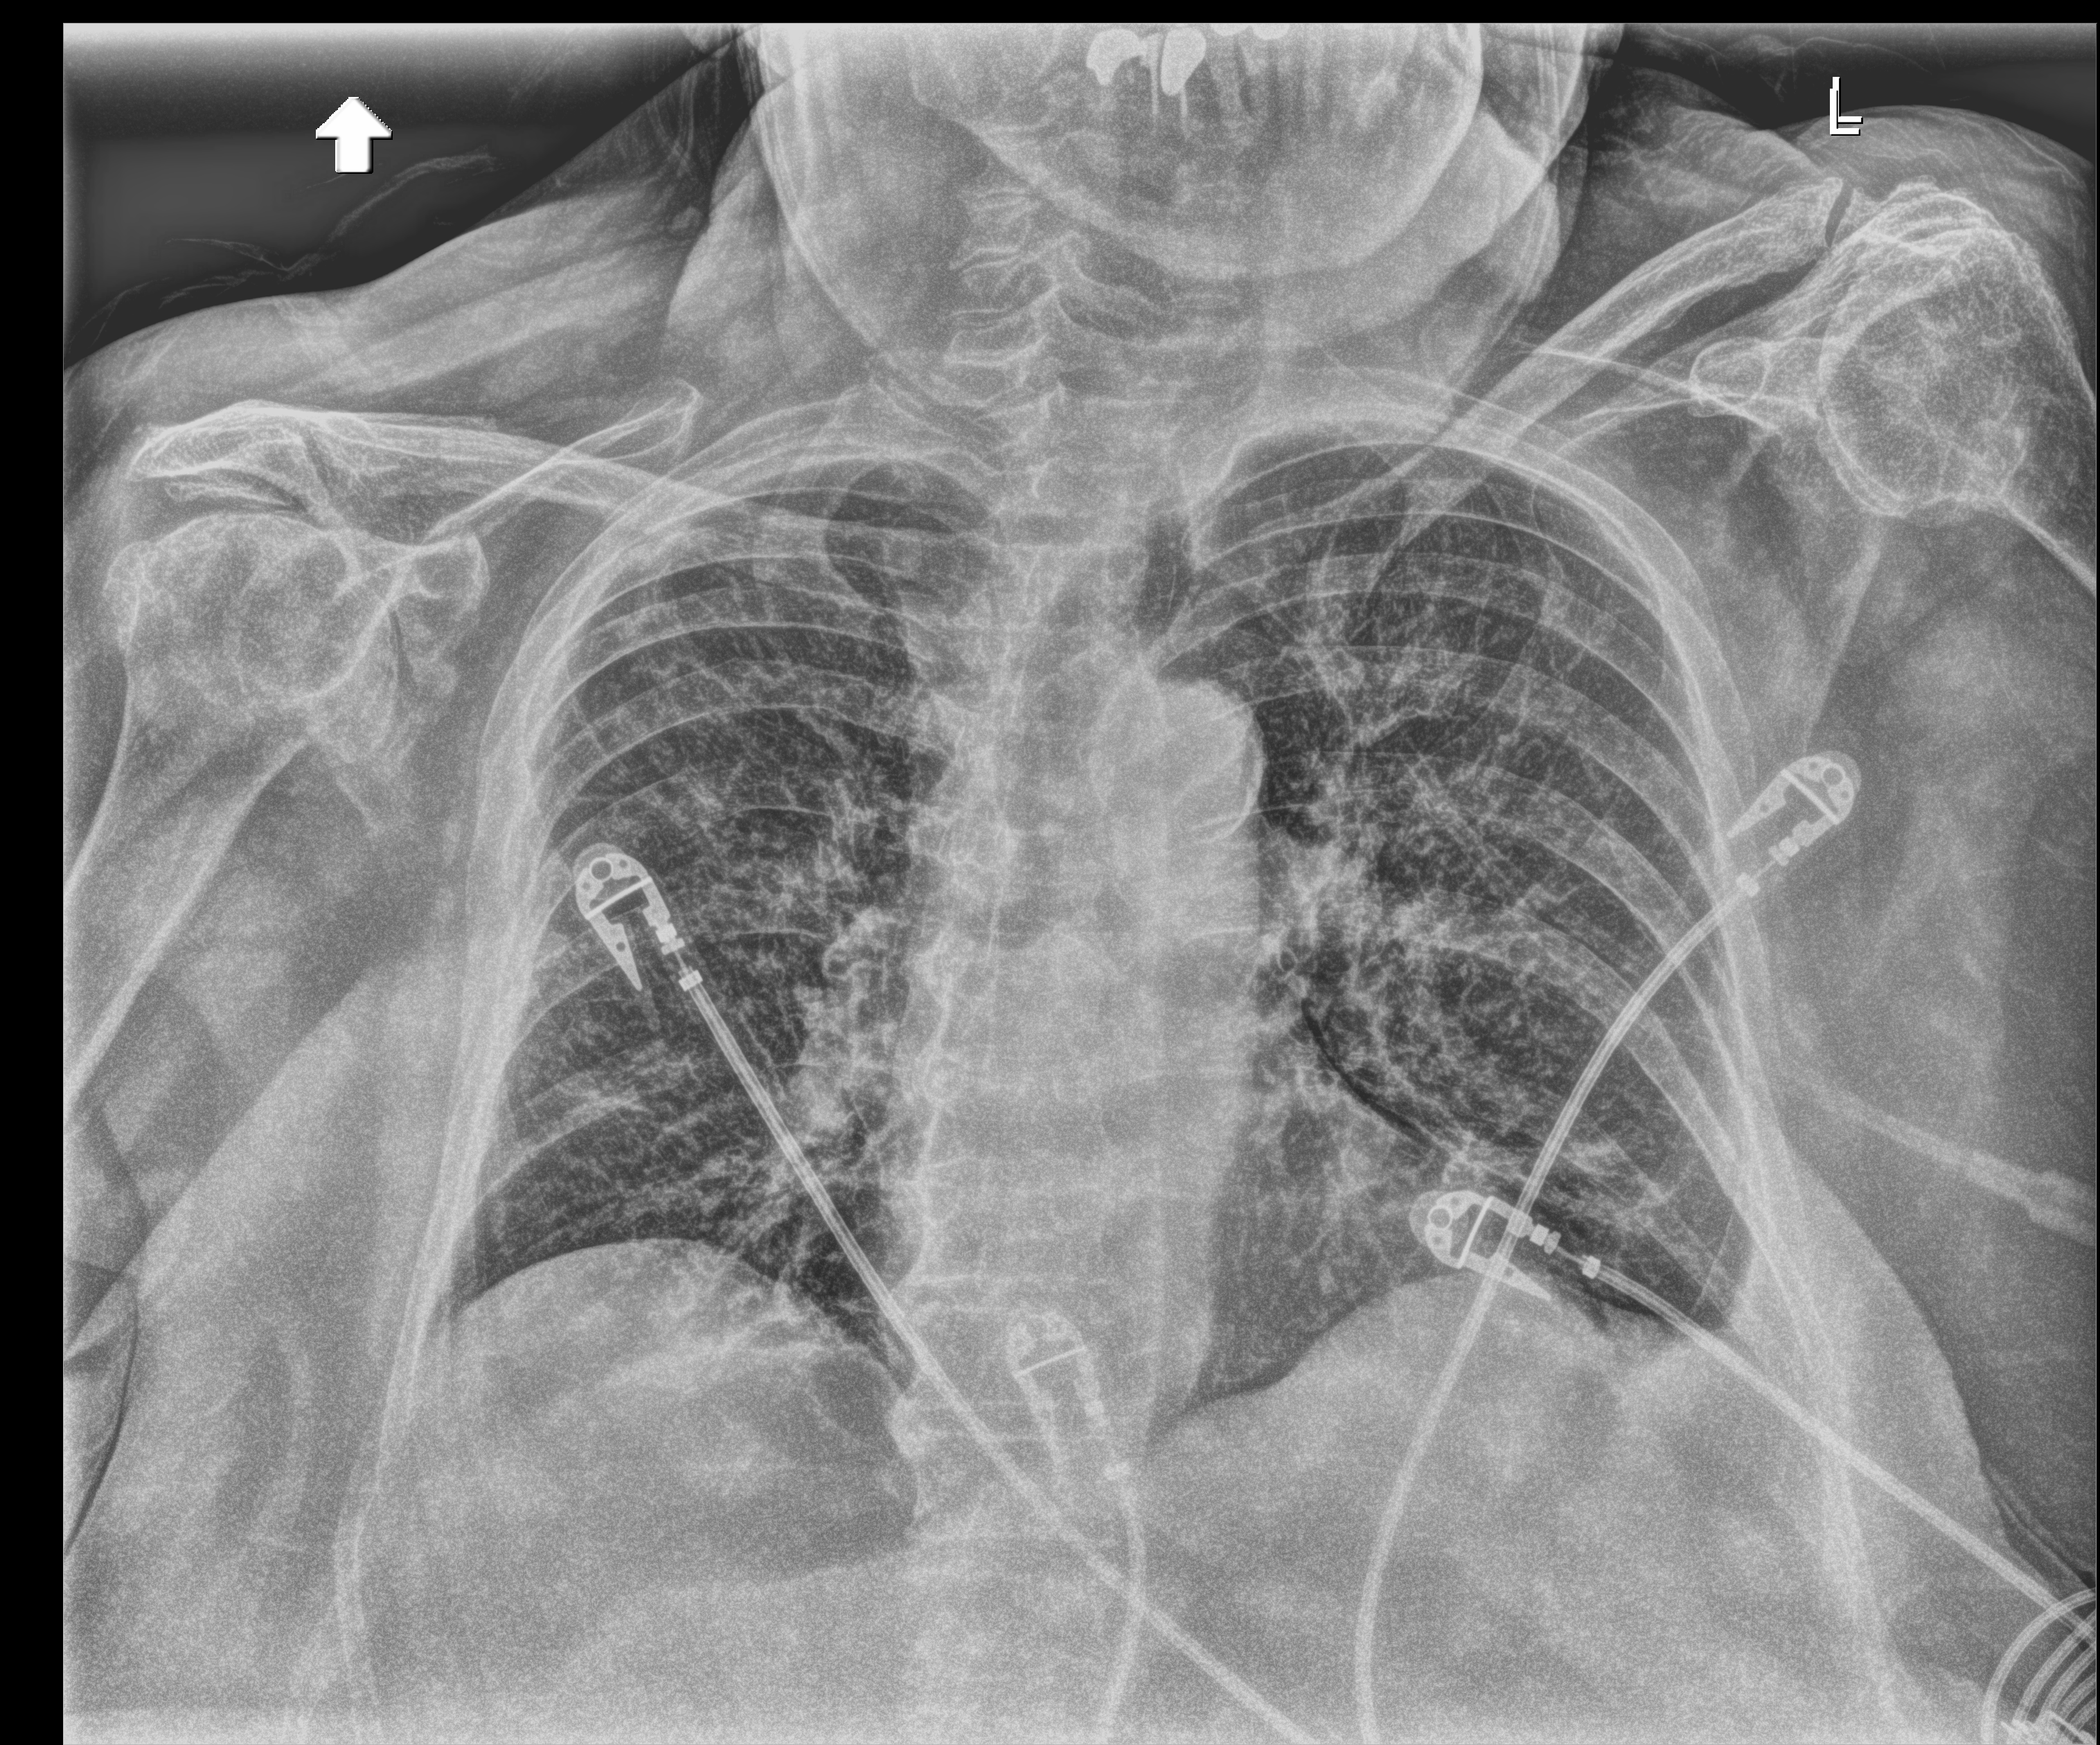
Chest X-ray (portable). Patient hospitalised with COVID-19; female, aged 75–90 years.
From the hospital-stay record, not from the radiograph (when in the stay this image was taken is not recorded): mechanically ventilated during this hospital stay: no; admitted to intensive care during this hospital stay: no.